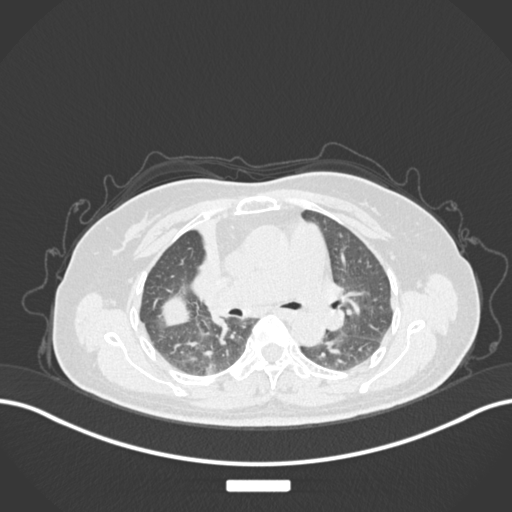
Chest CT, one axial slice. Reconstruction kernel B30f. 120 kVp. Lung window (W 1500 / L -600 HU). 1 mm slice thickness. 512 × 512 image matrix. Patient: female, 60 years. Case-level facts recorded for this patient, not image findings: clinical TNM (as recorded): T3 N1 M1.
Outlined on this slice (bounding box drawn by a radiologist):
- lung tumour (recorded histology: adenocarcinoma): bounding box <152,291,208,343> (left, top, right, bottom; pixels)